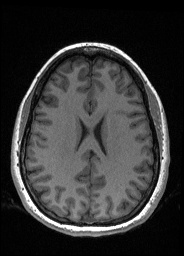
Pre-operative brain MRI before brain-tumour surgery, one axial slice. Slice 74 of 176 in the series (ordered by position). T1-weighted post-contrast. 1 mm slice thickness. 184 × 256 image matrix, field of view 180 × 250 mm. From the clinical record (not read from this slice): histopathology: Oligodendroglioma; WHO grade: 2; IDH mutation: yes; tumour location: Left Frontal.
Structures marked on this image (outlined manually by an expert reader):
- tumour: box from (x=100, y=113) to (x=106, y=118) px